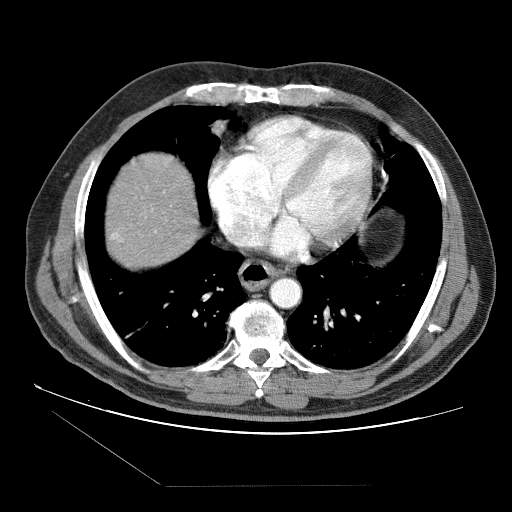
Contrast-enhanced abdominal CT (liver protocol), one axial slice; position 80 of 87 along the scan axis; reconstruction kernel STANDARD; 120 kVp; soft-tissue window (W 400 / L 40 HU); 2.5 mm slice thickness; 512 × 512 image matrix. From the clinical record (not read from this slice): diagnosis: hepatocellular carcinoma (patient treated with transarterial chemoembolisation; whether this scan precedes or follows treatment is not stated here); TNM stage (as recorded): Stage-II; Child-Pugh class: B; tumour differentiation: no biopsy; tumour size: 2.6 cm.
Annotated regions visible in this slice (semi-automatically segmented with operator editing):
- liver parenchyma outside the tumour (the mass and vessels are separate outlines, so this box may not span the whole liver): bounding box (x1, y1, x2, y2) in pixels: (106, 152, 198, 266)
- liver vessels: (112, 233, 118, 238)